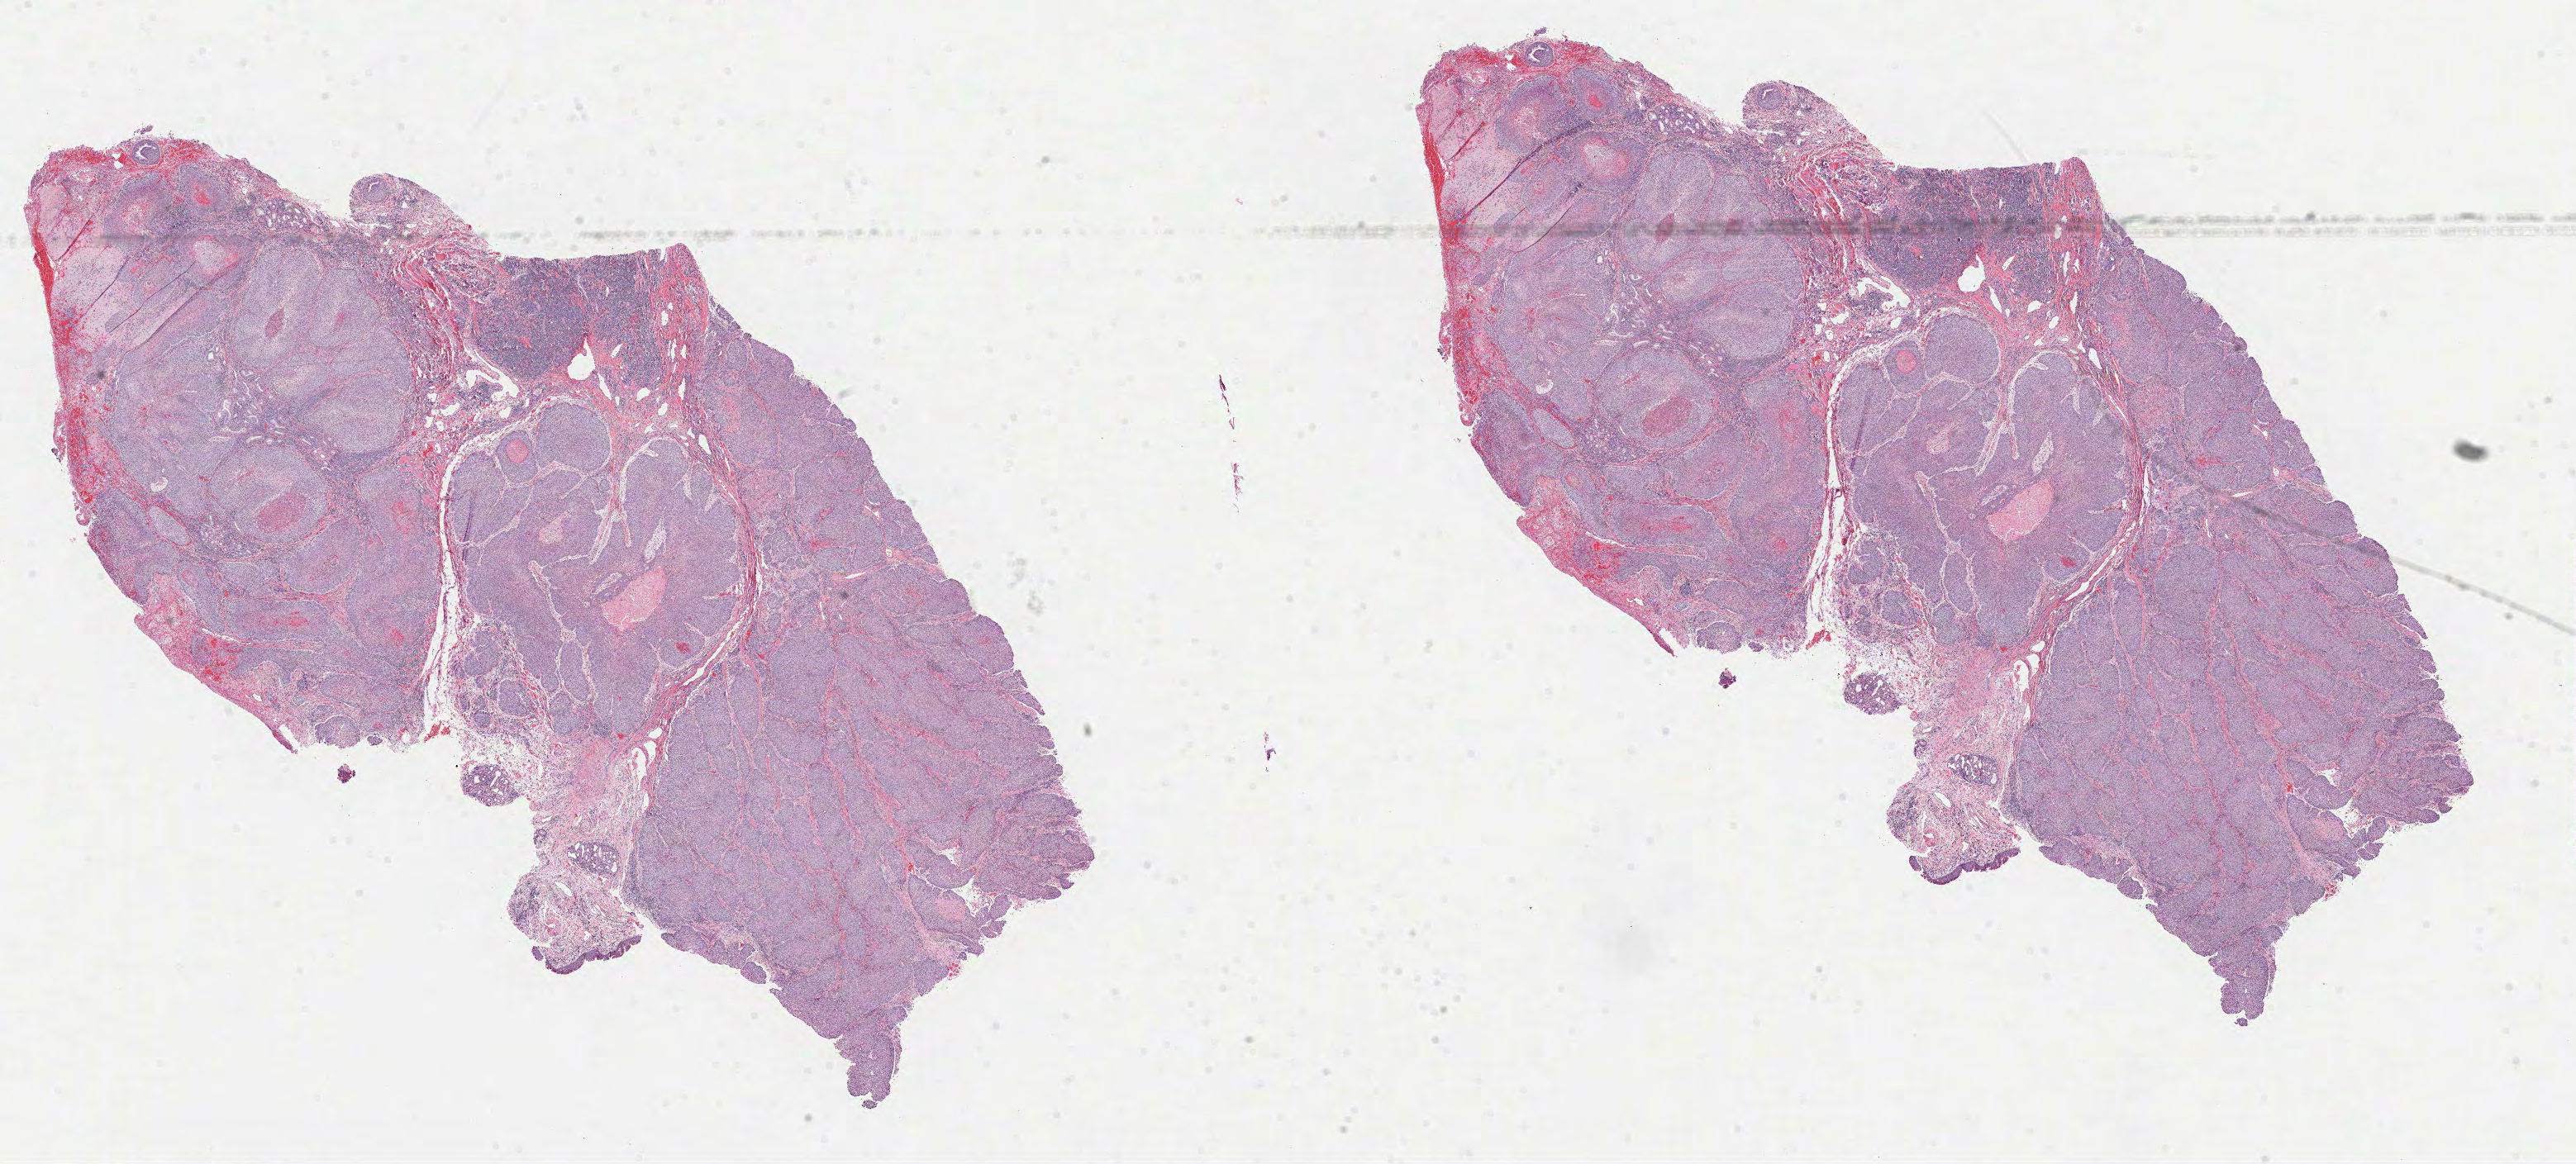
Whole-slide histology image, Hematoxylin and eosin (H&E) stained, whole scanned area (about 25.1 x 11.4 mm) shown as a low-resolution overview; formalin-fixed paraffin-embedded (FFPE) diagnostic section; primary tumour sample from the head and neck. Male, age 68 years at initial diagnosis. Histologic grade: G2 (moderately differentiated).
- AJCC pathologic stage: IVA (6th edition)
- TNM: T4a N0 M0
- diagnosis: Squamous cell carcinoma, NOS (larynx, NOS)